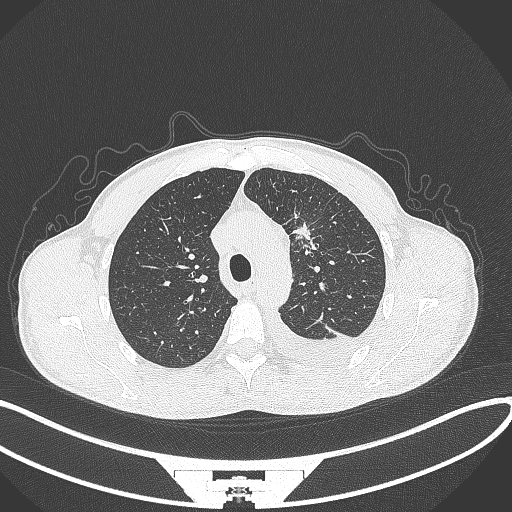
Chest CT, one axial slice; position 244 of 371 along the scan axis; reconstruction kernel B70f; lung window (W 1500 / L -600 HU); 1 mm slice thickness; 512 × 512 image matrix, field of view 400 × 400 mm. Patient: male, 49 years. From the clinical record (not read from this slice): clinical TNM (as recorded): T1c N1 M1.
Outlined on this slice (bounding box drawn by a radiologist):
- lung tumour (recorded histology: adenocarcinoma): bounding box <294,214,320,257> (left, top, right, bottom; pixels)